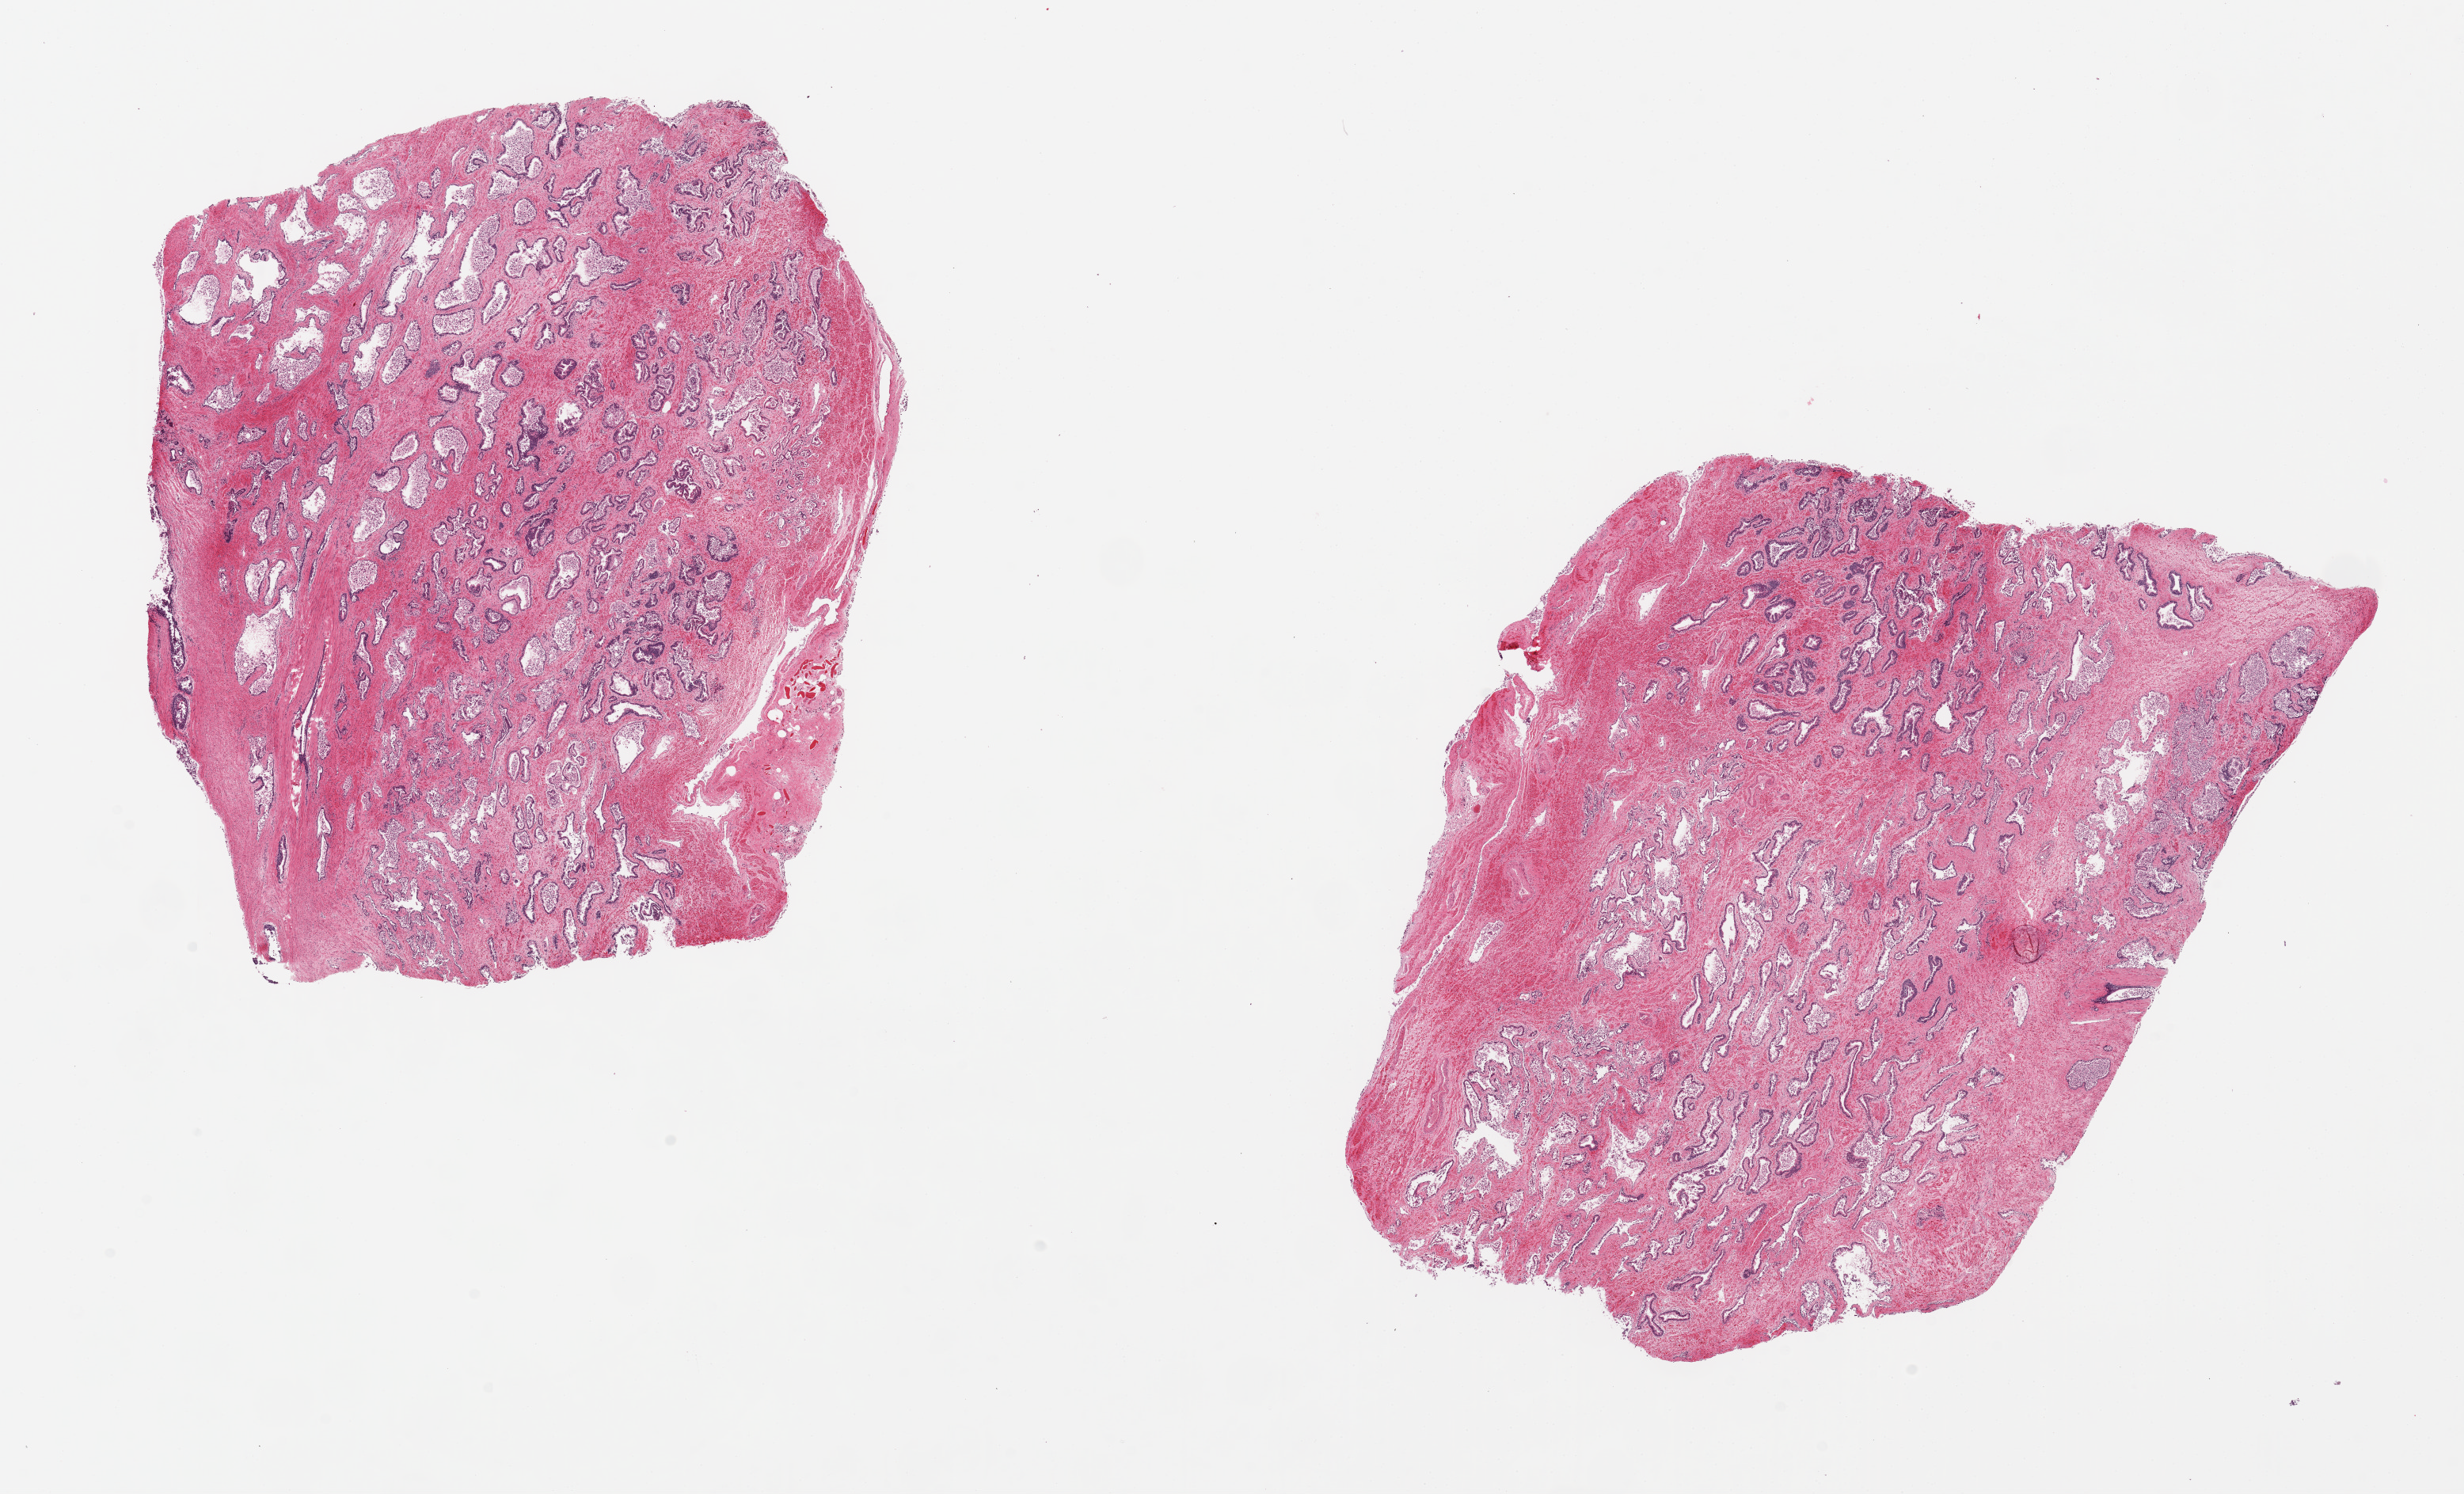
Whole-slide image, haematoxylin and eosin stain, brightfield — shown as a low-resolution overview of the whole scanned area (about 24.6 x 14.9 mm). PAXgene-fixed, paraffin-embedded tissue. Section of prostate (target tissue). Donor tissue sample. Male donor.
- pathologist's review note for this sample: 2 pieces; 8.5x8 & 10x8mm; glands moderately autolyzed; one better preserved (~grade 1) area